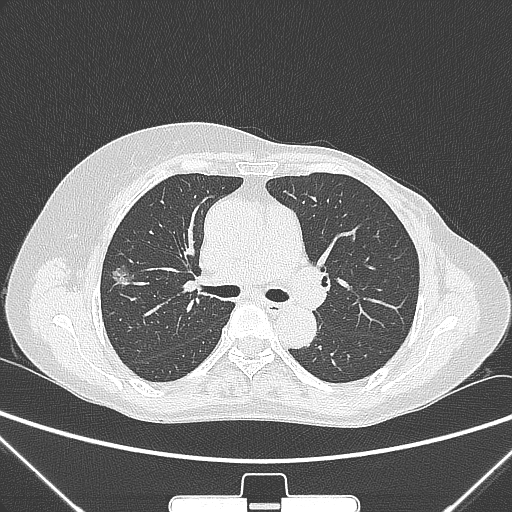
Chest CT, one axial slice; slice 157 of 265 in the series (ordered by position); 120 kVp; lung window (W 1500 / L -600 HU); 512 × 512 image matrix, field of view 350 × 350 mm. Female patient, age 64 years. Case-level facts recorded for this patient, not image findings: clinical TNM (as recorded): T1c N0 M0; histopathological grade: G1-2.
Structures marked on this image (rectangle marked by the reading radiologist):
- lung tumour (recorded histology: adenocarcinoma): bounding box [x1, y1, x2, y2] px = [108, 264, 139, 292]